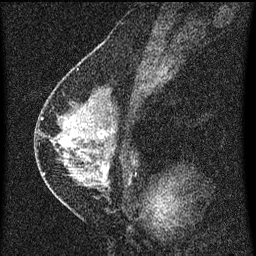
Breast MRI (dynamic contrast-enhanced), one sagittal slice. Position 31 of 60 along the scan axis. Dynamic contrast-enhanced series, image 2 of 3 at this slice position (ordered by acquisition). 1.5 T. TE 4.2 ms, TR 8 ms. 2 mm slice thickness. 256 × 256 image matrix, field of view 180 × 180 mm. Patient: female, 47 years.
Outlined on this slice (semi-automatic segmentation, software-assisted and operator-edited):
- analysis volume of interest (the breast-tissue region the enhancement analysis was run in; not a lesion): box from (x=42, y=92) to (x=140, y=199) px
- tumour enhancement mask (voxels above the 70 % enhancement threshold inside the analysis volume of interest): (x=43, y=132)–(x=109, y=177)